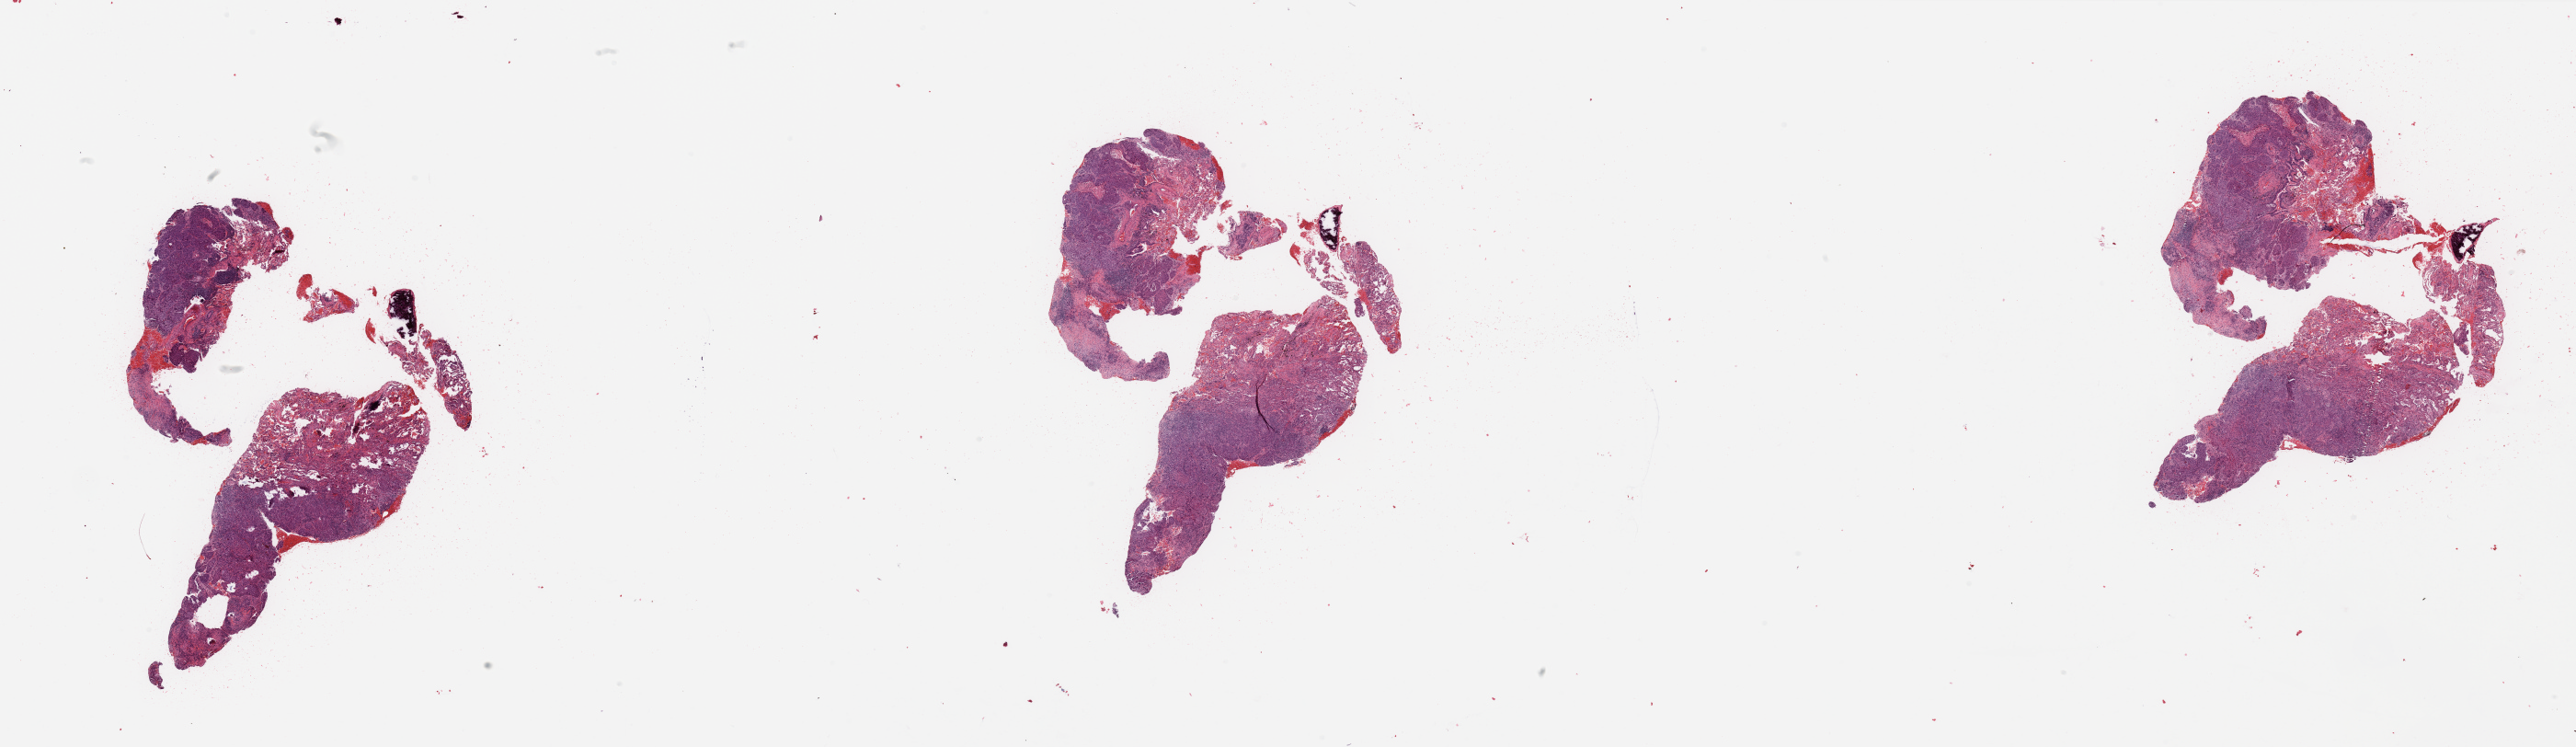
Hematoxylin and eosin (H&E) stained whole-slide image, whole scanned area (about 44.3 x 12.8 mm, slide scanned at 20x) shown as a low-resolution overview. Tumour tissue sample, sampled site: lung. Female, 68 y/o. Histologic grade: G3 (poorly differentiated). Slide review estimates, as recorded: tumour nuclei 70%, necrosis 5%.
- histologic diagnosis: Squamous cell carcinoma, NOS
- primary tumour site (as recorded): left upper lobe